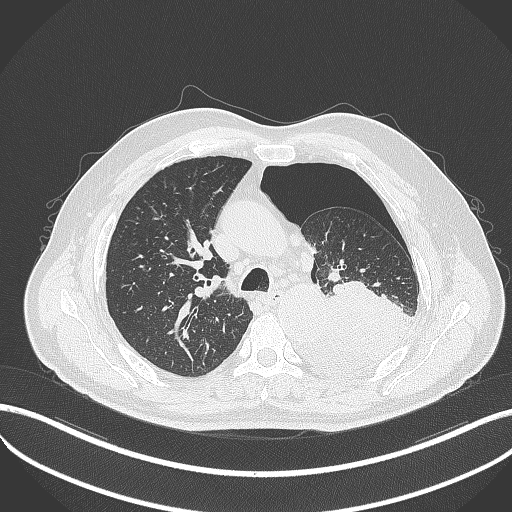
Chest CT, one axial slice. Slice 354 of 464 in the series (ordered by position). Reconstruction kernel B70f. Lung window (W 1500 / L -600 HU). 1 mm slice thickness. 512 × 512 image matrix, field of view 400 × 400 mm. Patient: male, 76 years. From the clinical record (not read from this slice): clinical TNM (as recorded): T3 N0 M1b.
Annotated regions visible in this slice (bounding box drawn by a radiologist):
- lung tumour (recorded histology: adenocarcinoma): bounding box <283,276,415,383> (left, top, right, bottom; pixels)